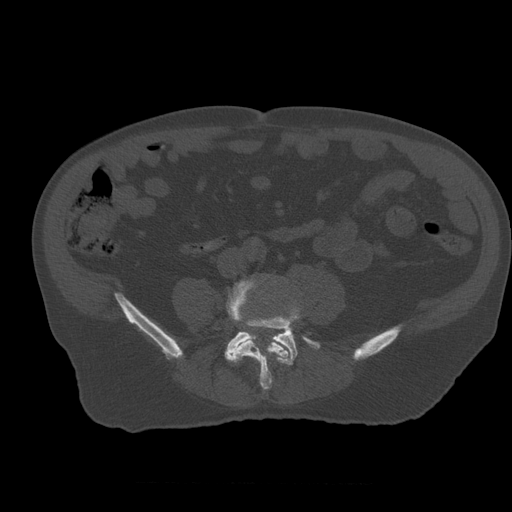
CT including the spine, one axial slice. Slice 153 of 399 in the series (ordered by position). Reconstruction kernel STANDARD. 120 kVp. Bone window (W 1800 / L 400 HU). 1.25 mm slice thickness. 512 × 512 image matrix, field of view 407 × 407 mm. Patient age 73 years. From the clinical record (not read from this slice): primary cancer: prostate; vertebrae with lytic lesions (as recorded): L2.
Annotated regions visible in this slice (semi-automatic segmentation, software-assisted and operator-edited):
- L4 vertebra: bounding box [x1, y1, x2, y2] px = [228, 279, 289, 391]
- L5 vertebra: [225, 315, 320, 366]